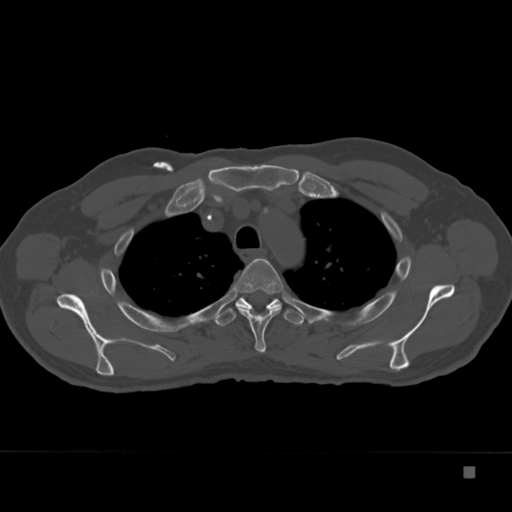
CT including the spine, one axial slice; slice 280 of 332 in the series (ordered by position); reconstruction kernel Br40s; bone window (W 1800 / L 400 HU); 1.5 mm slice thickness; 512 × 512 image matrix, field of view 389 × 389 mm. Male patient, age 72 years. Case-level facts recorded for this patient, not image findings: primary cancer: skeletal.
Structures marked on this image (semi-automatically segmented with operator editing):
- T3 vertebra: box from (x=233, y=258) to (x=284, y=353) px
- T4 vertebra: (x=214, y=297)–(x=306, y=326)